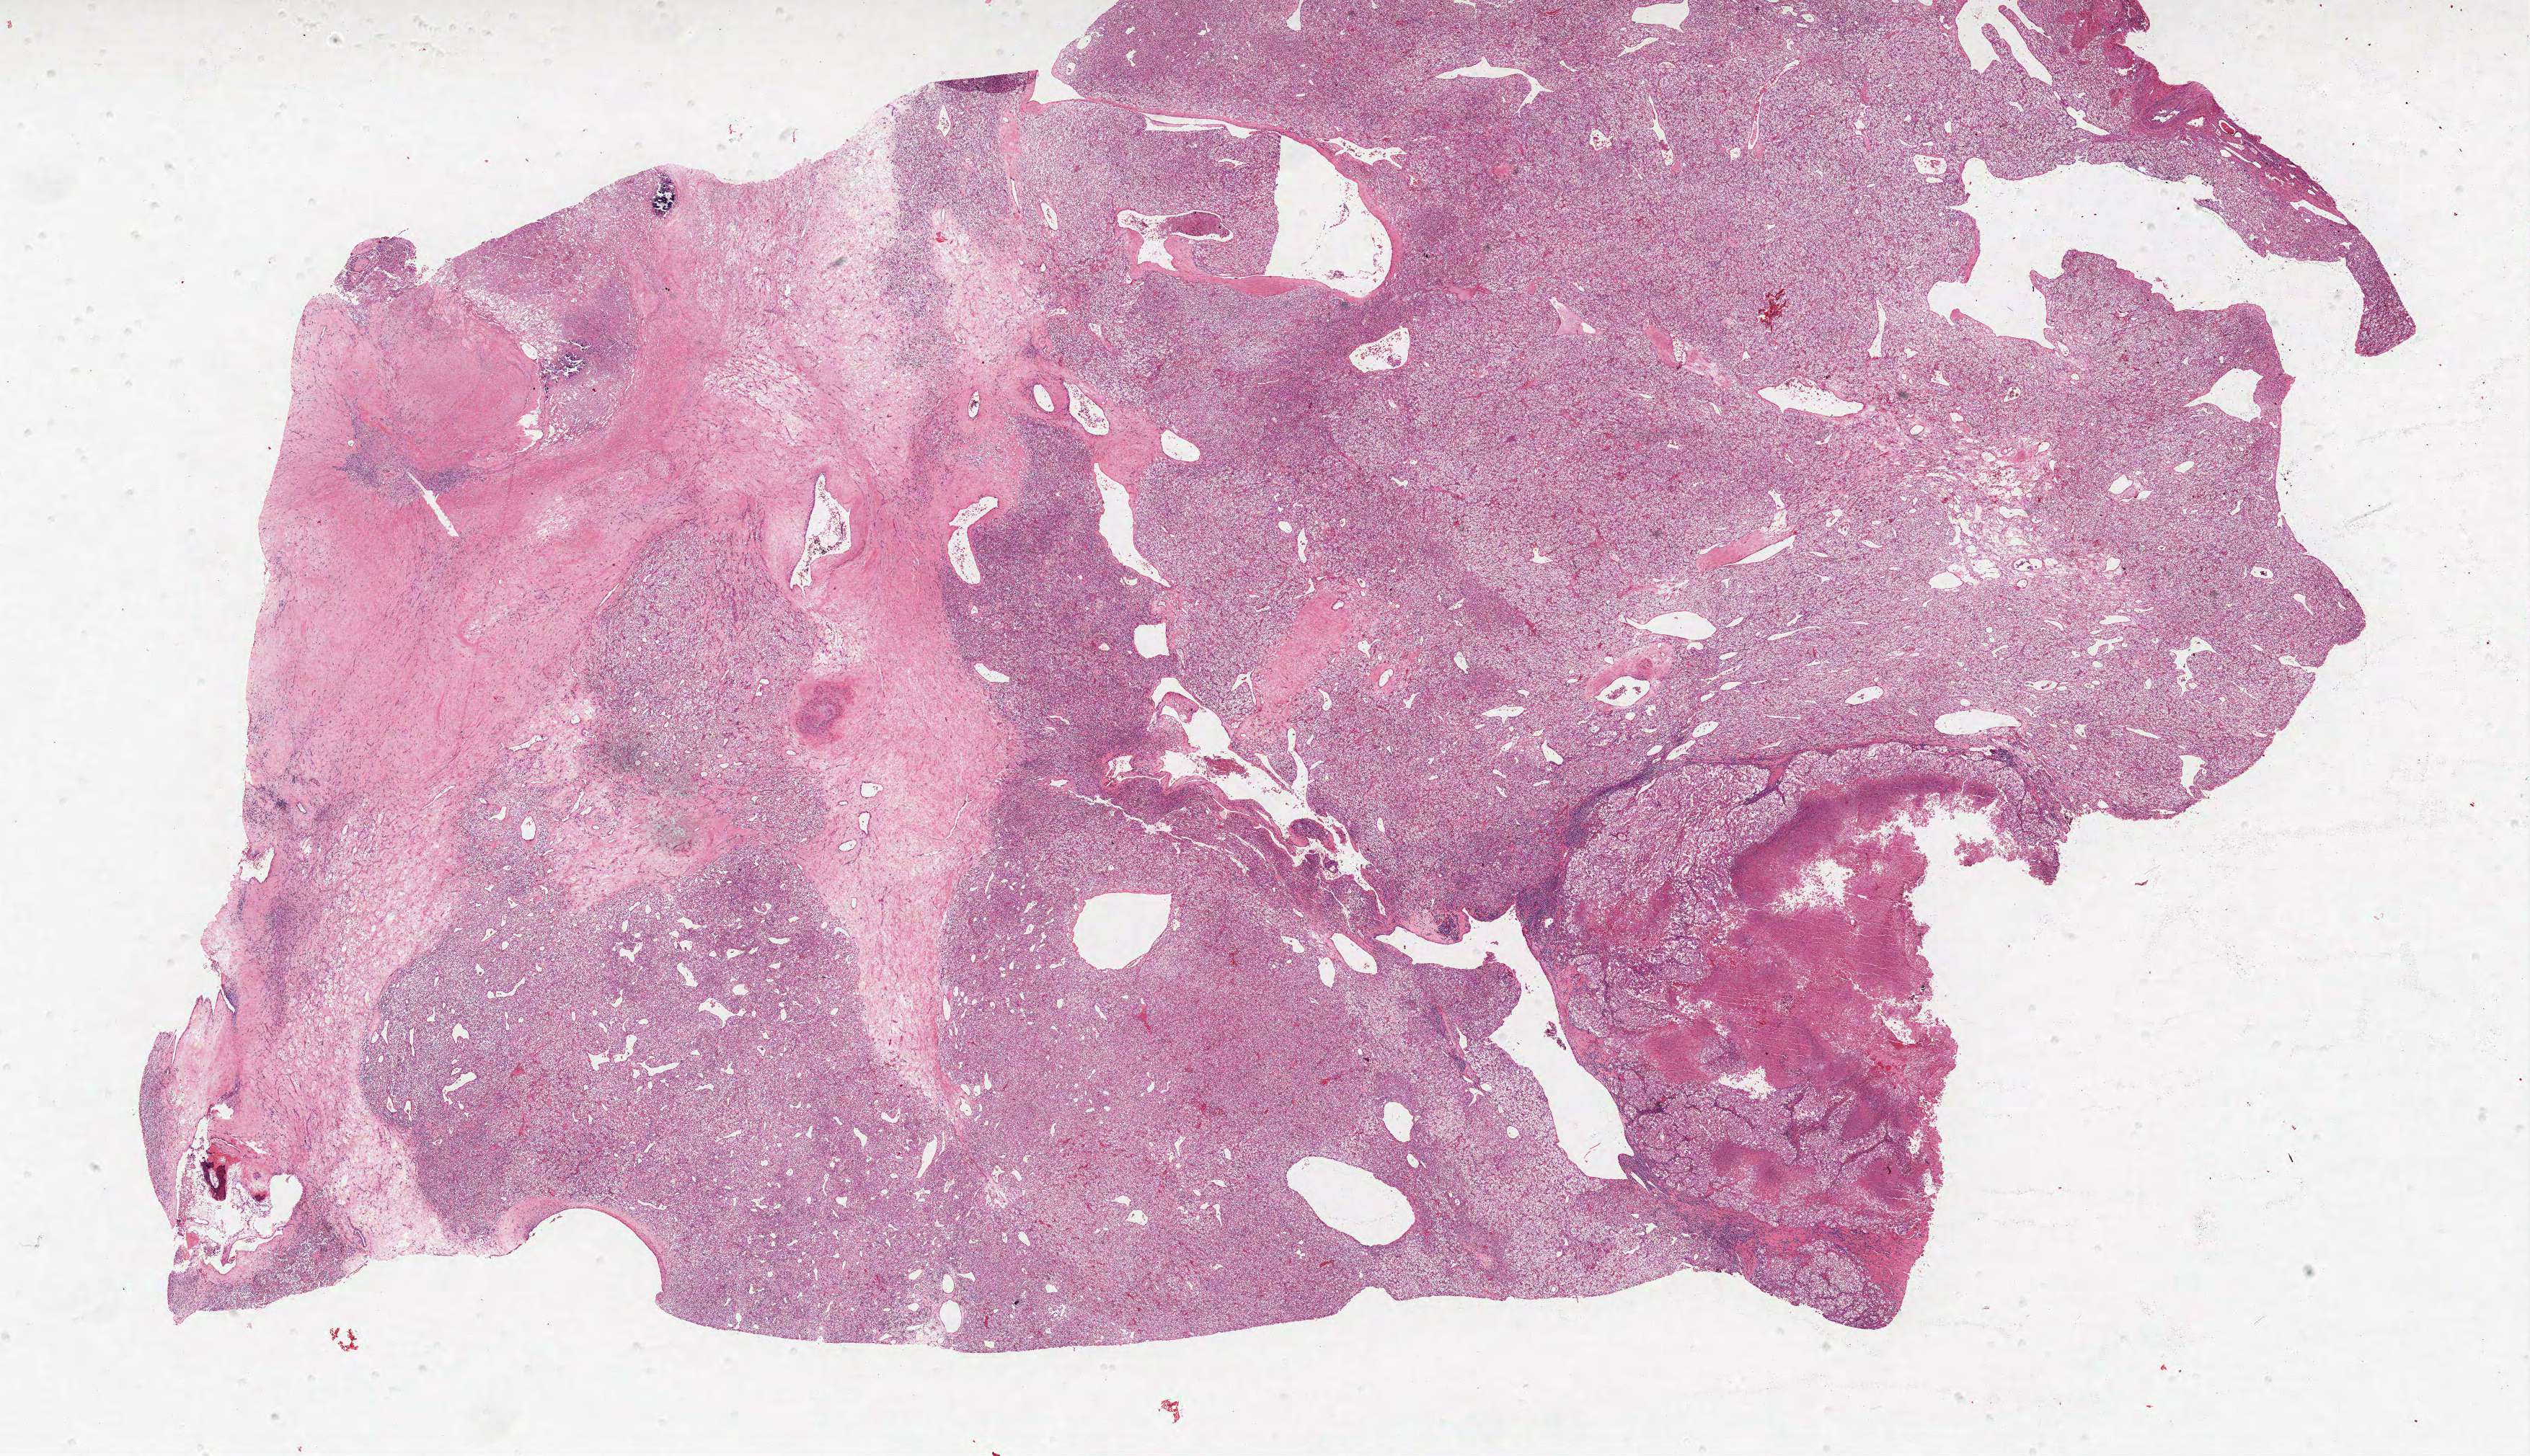
Digitized H&E-stained tissue section (whole slide) — whole scanned area (about 28.1 x 16.1 mm, slide scanned at 40x) shown as a low-resolution overview. FFPE section. Kidney, primary tumour sample. Female, age 65 years at initial diagnosis. Histologic grade: G3 (poorly differentiated).
* histologic diagnosis: Clear cell adenocarcinoma, NOS
* AJCC pathologic stage: IV
* laterality: left